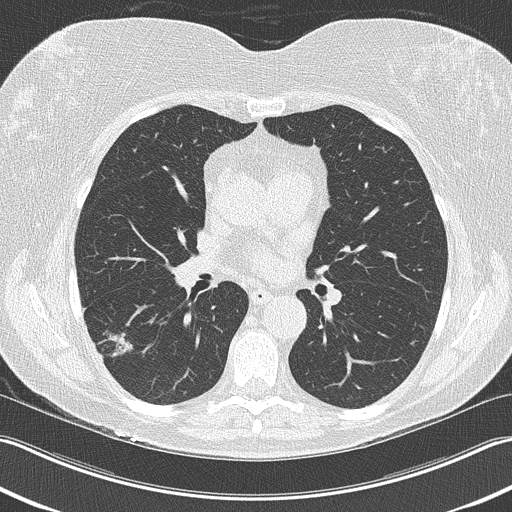
Low-dose screening chest CT, one axial slice; slice 123 of 210 in the series (ordered by position); reconstruction kernel B50f; 120 kVp; lung window (W 1500 / L -600 HU); 2 mm slice thickness; 512 × 512 image matrix, field of view 348 × 348 mm.
Outlined on this slice (manually delineated by an expert):
- lesion 1 (tumor, lower lobe of right lung): bounding box (x1, y1, x2, y2) in pixels: (103, 323, 133, 357)